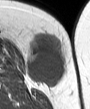
MRI of an extremity soft-tissue mass, one axial slice; position 13 of 45 along the scan axis; MR volume resampled by the dataset authors to the PET/CT grid (not the native acquisition matrix); 3.27 mm slice thickness; 90 × 109 image matrix, field of view 88 × 106 mm. Female patient. Case-level facts recorded for this patient, not image findings: histological type: leiomyosarcoma; grade: intermediate; site of the primary tumour: parascapusular.
Outlined on this slice (expert contour drawn on MRI and transferred to this co-registered scan by the dataset authors):
- gross tumour volume including surrounding oedema: box from (x=26, y=34) to (x=66, y=88) px
- gross tumour volume (mass): (x=26, y=34)–(x=66, y=86)